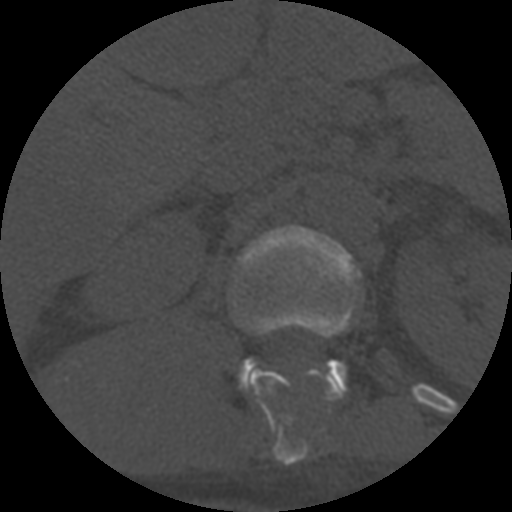
CT including the spine, one axial slice; position 301 of 708 along the scan axis; reconstruction kernel STANDARD; 120 kVp; one of 3 acquisitions stored at this slice position; bone window (W 1800 / L 400 HU); 512 × 512 image matrix, field of view 160 × 160 mm. Patient age 55 years. From the clinical record (not read from this slice): primary cancer: colon; vertebrae with lytic lesions (as recorded): T12, L1, L5.
Outlined on this slice (semi-automatically segmented with operator editing):
- L1 vertebra: bounding box (x1, y1, x2, y2) in pixels: (240, 226, 359, 400)
- T12 vertebra: (250, 370, 332, 465)